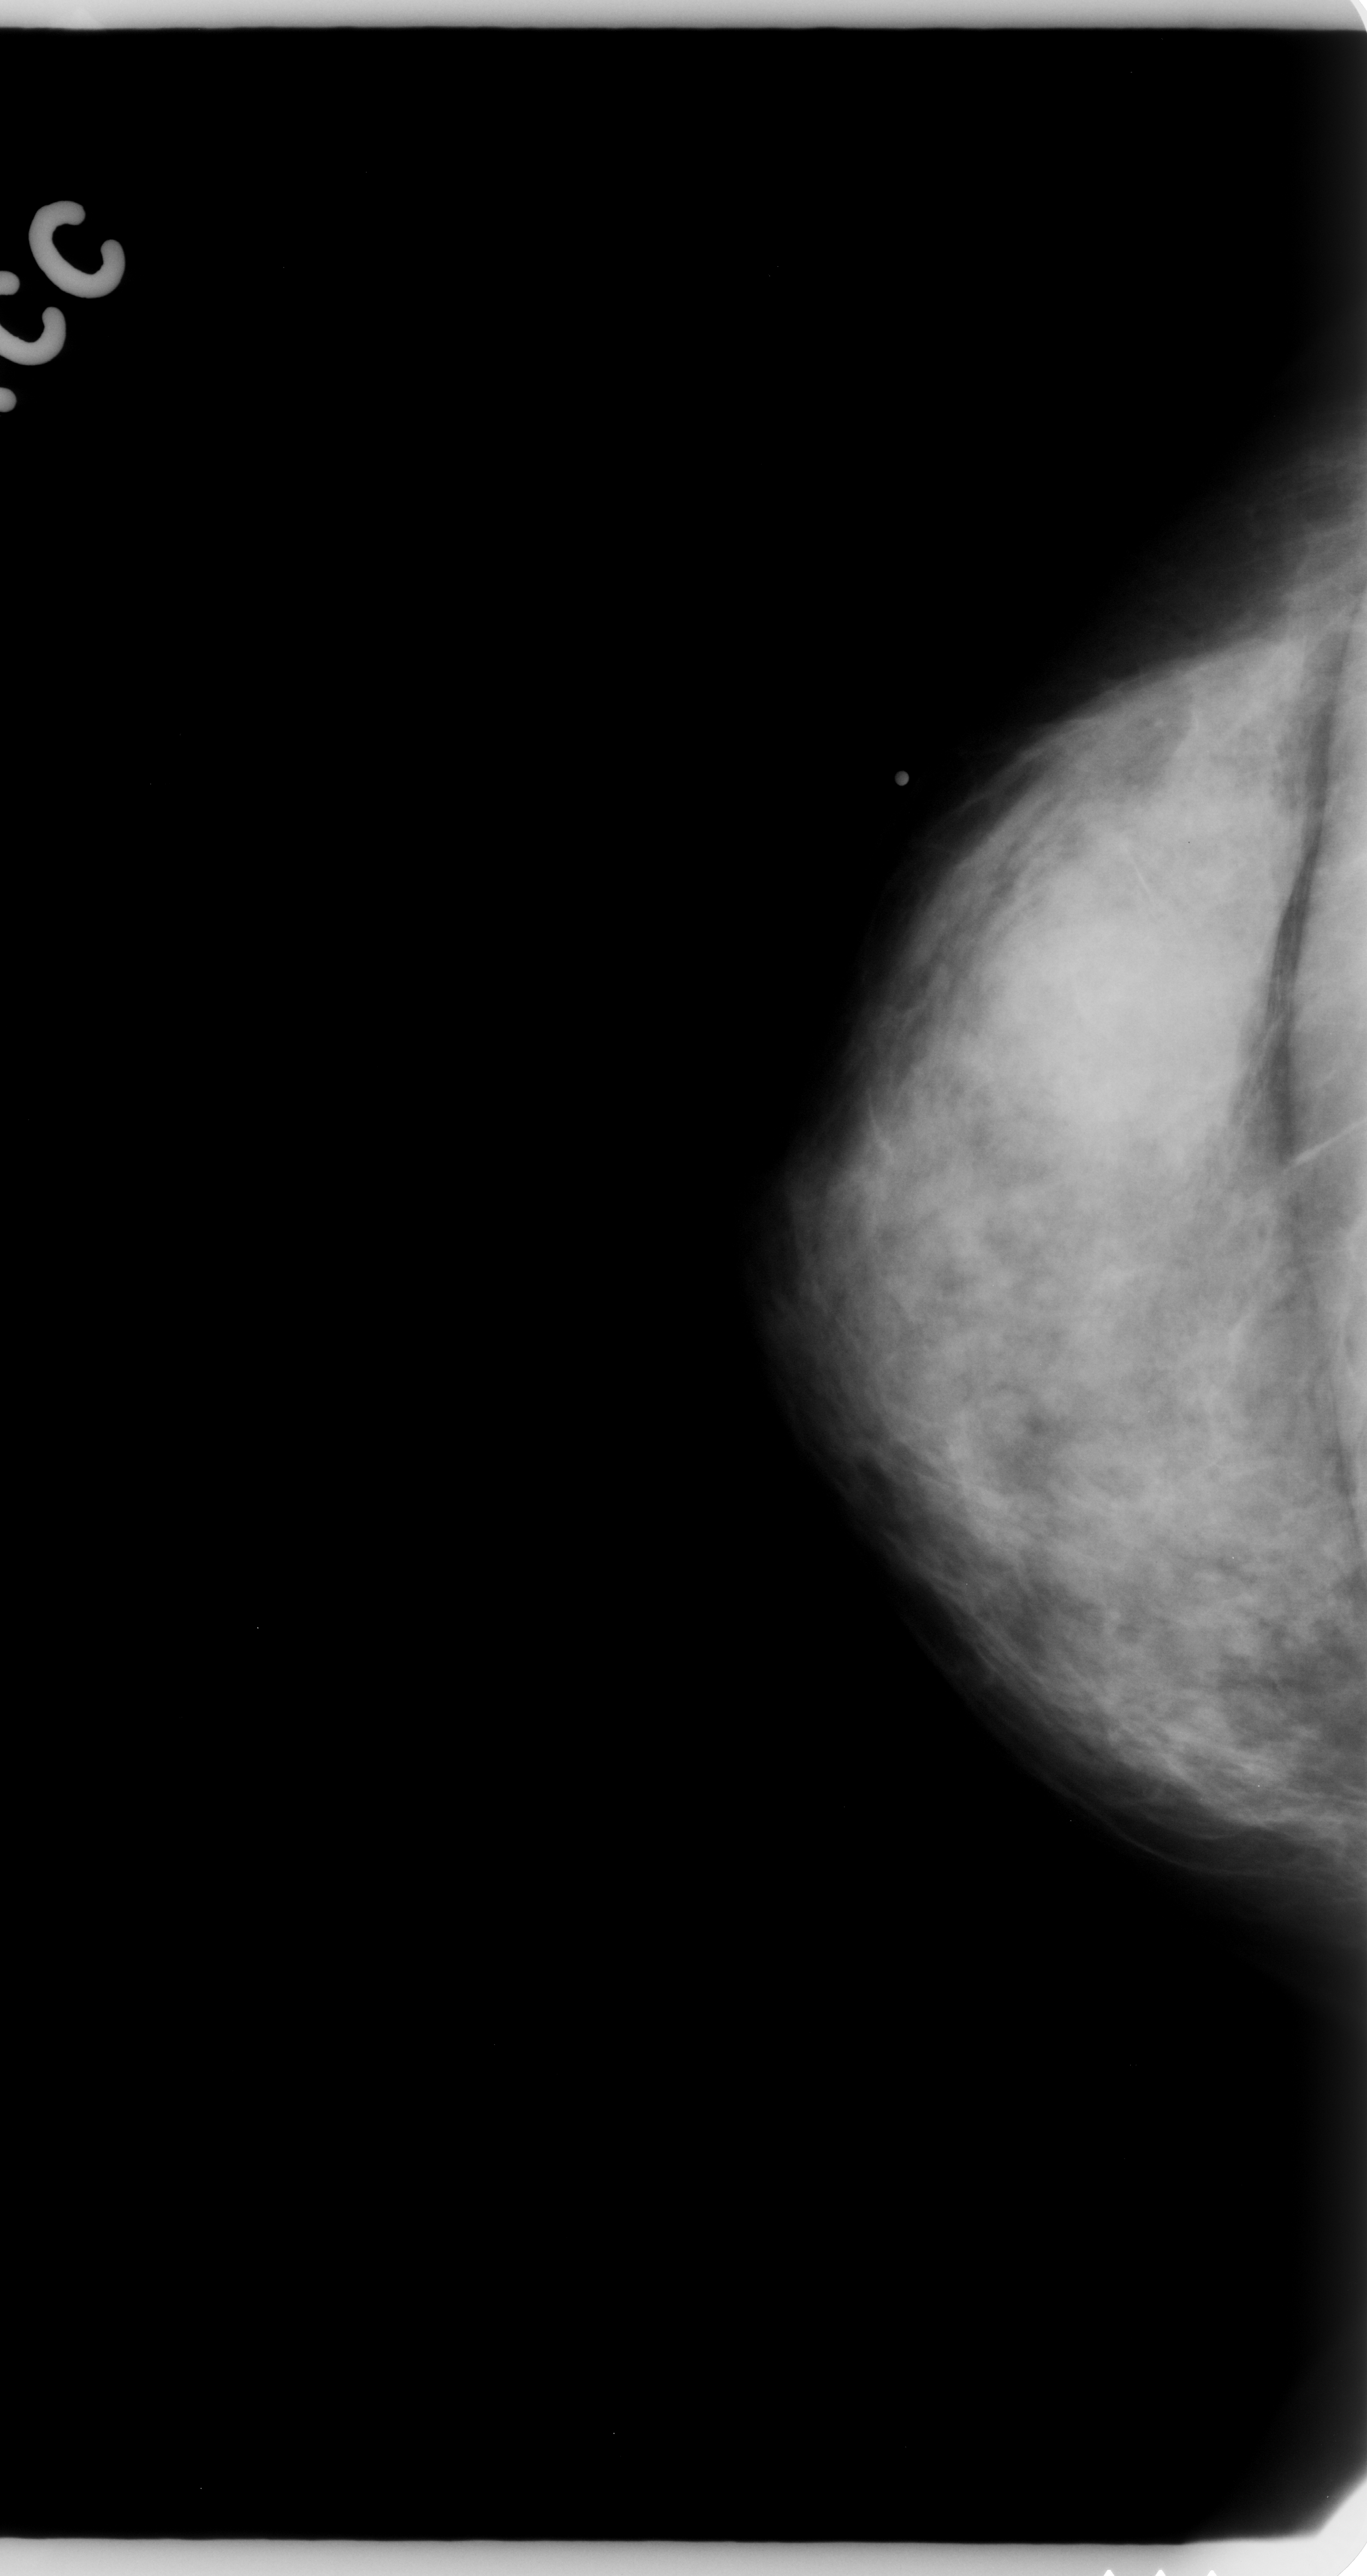
Scanned film-screen mammogram. Right breast. CC view. 1367 × 2576 image matrix.
Expert-marked regions of interest on this film, with their recorded descriptors:
- mass, shape round, margins ill defined; BI-RADS assessment category 4; subtlety rating 3 on a 1 (subtle) to 5 (obvious) scale; pathology result (as recorded, not read from the image): malignant: box from (x=962, y=872) to (x=1269, y=1170) px